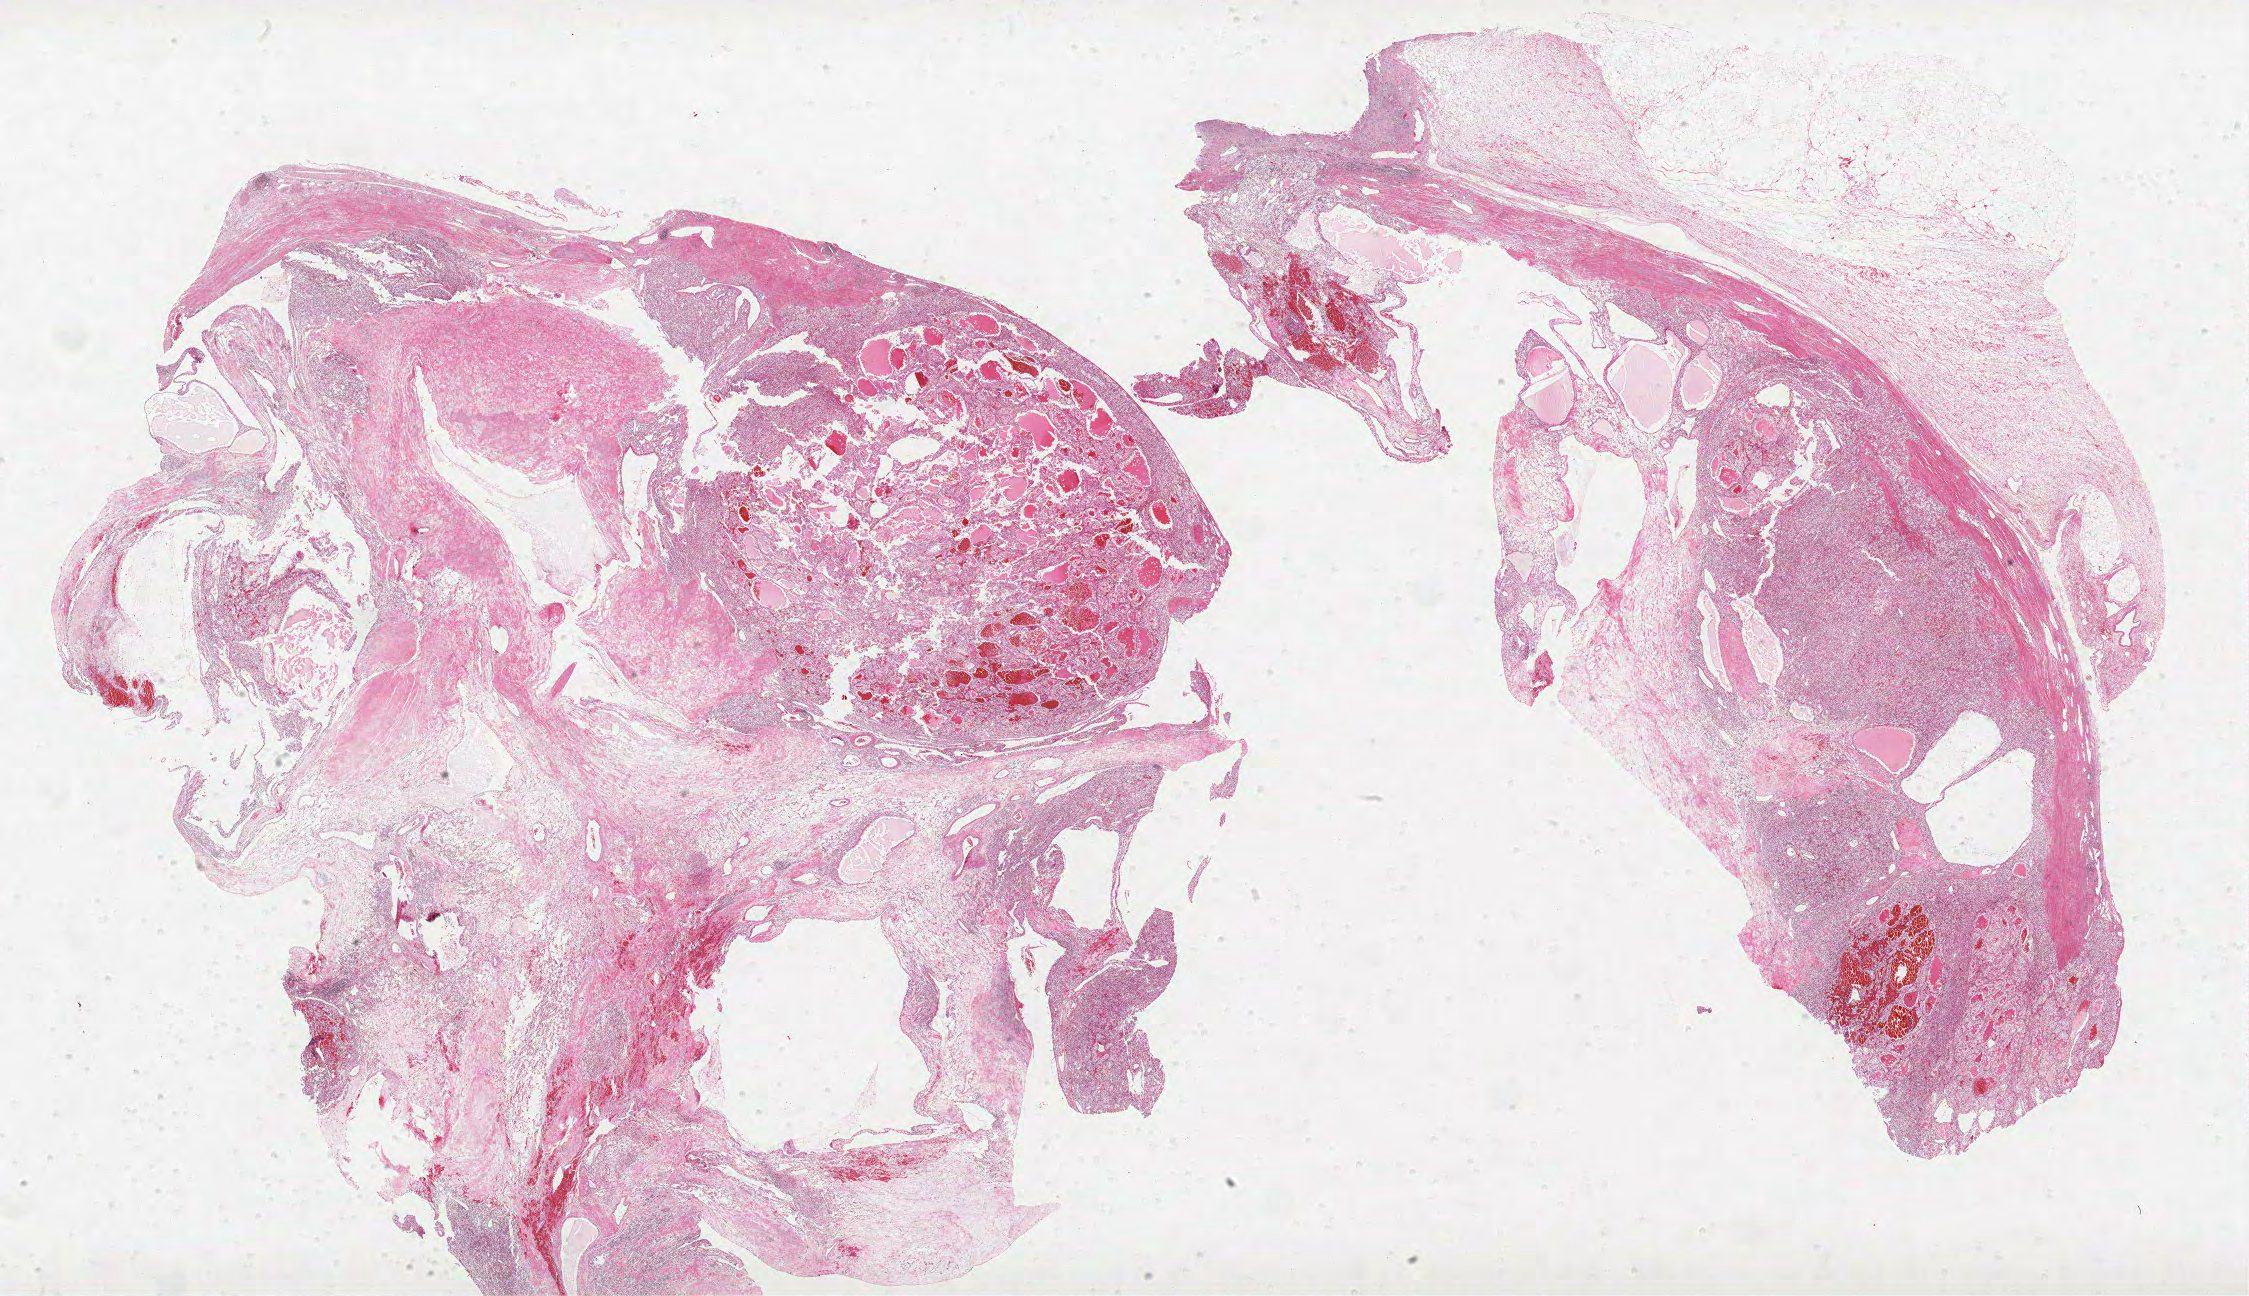
Digitized H&E-stained tissue section (whole slide) — a low-resolution overview of the entire scanned area, about 36.0 x 20.7 mm (acquisition: 40x scan), FFPE section, primary tumour sample from the kidney. Male patient; age at initial diagnosis 57 years. Histologic grade: G3 (poorly differentiated).
TNM: T1b NX M0. AJCC pathologic stage: I. Histologic diagnosis: Clear cell adenocarcinoma, NOS. Laterality: left.